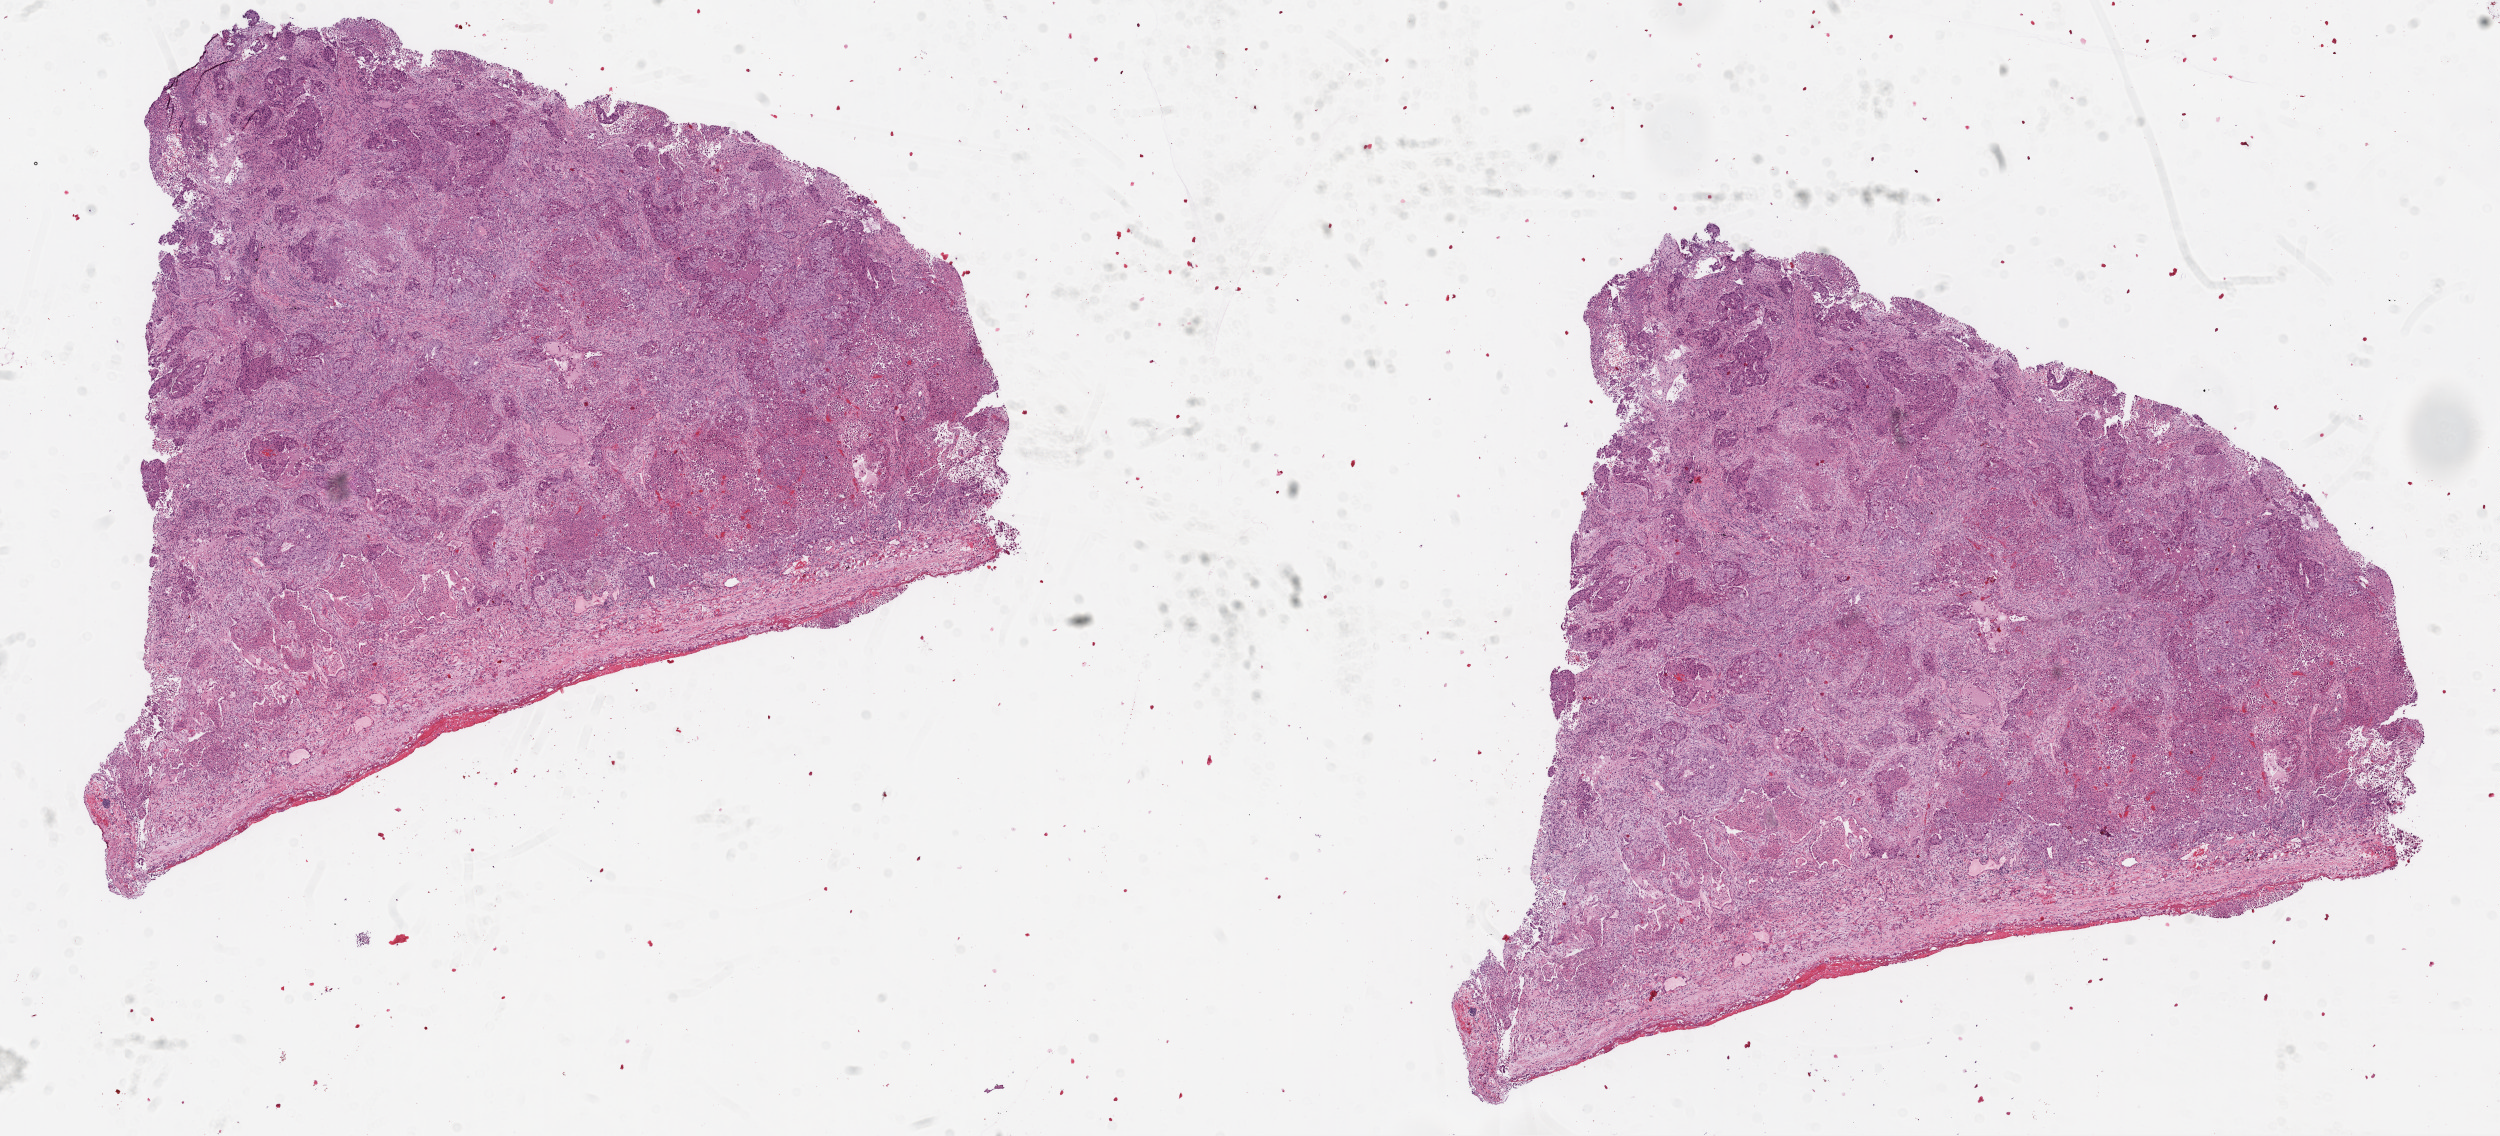
Whole-slide histology image, H&E, shown as a low-resolution overview of the whole scanned area (about 20.1 x 9.1 mm, from a 20x scan), frozen section from the top of the tissue portion, primary tumour sample from the lung. Patient: male, age at initial diagnosis 65 years. Slide review estimates, as recorded: tumour cells 80%, tumour nuclei 80%, normal cells 0%, stromal cells 12%, necrosis 8%. Infiltration values recorded for this section: lymphocyte infiltration 5%.
- diagnosis: Adenocarcinoma, NOS
- AJCC pathologic stage: IB (6th edition)